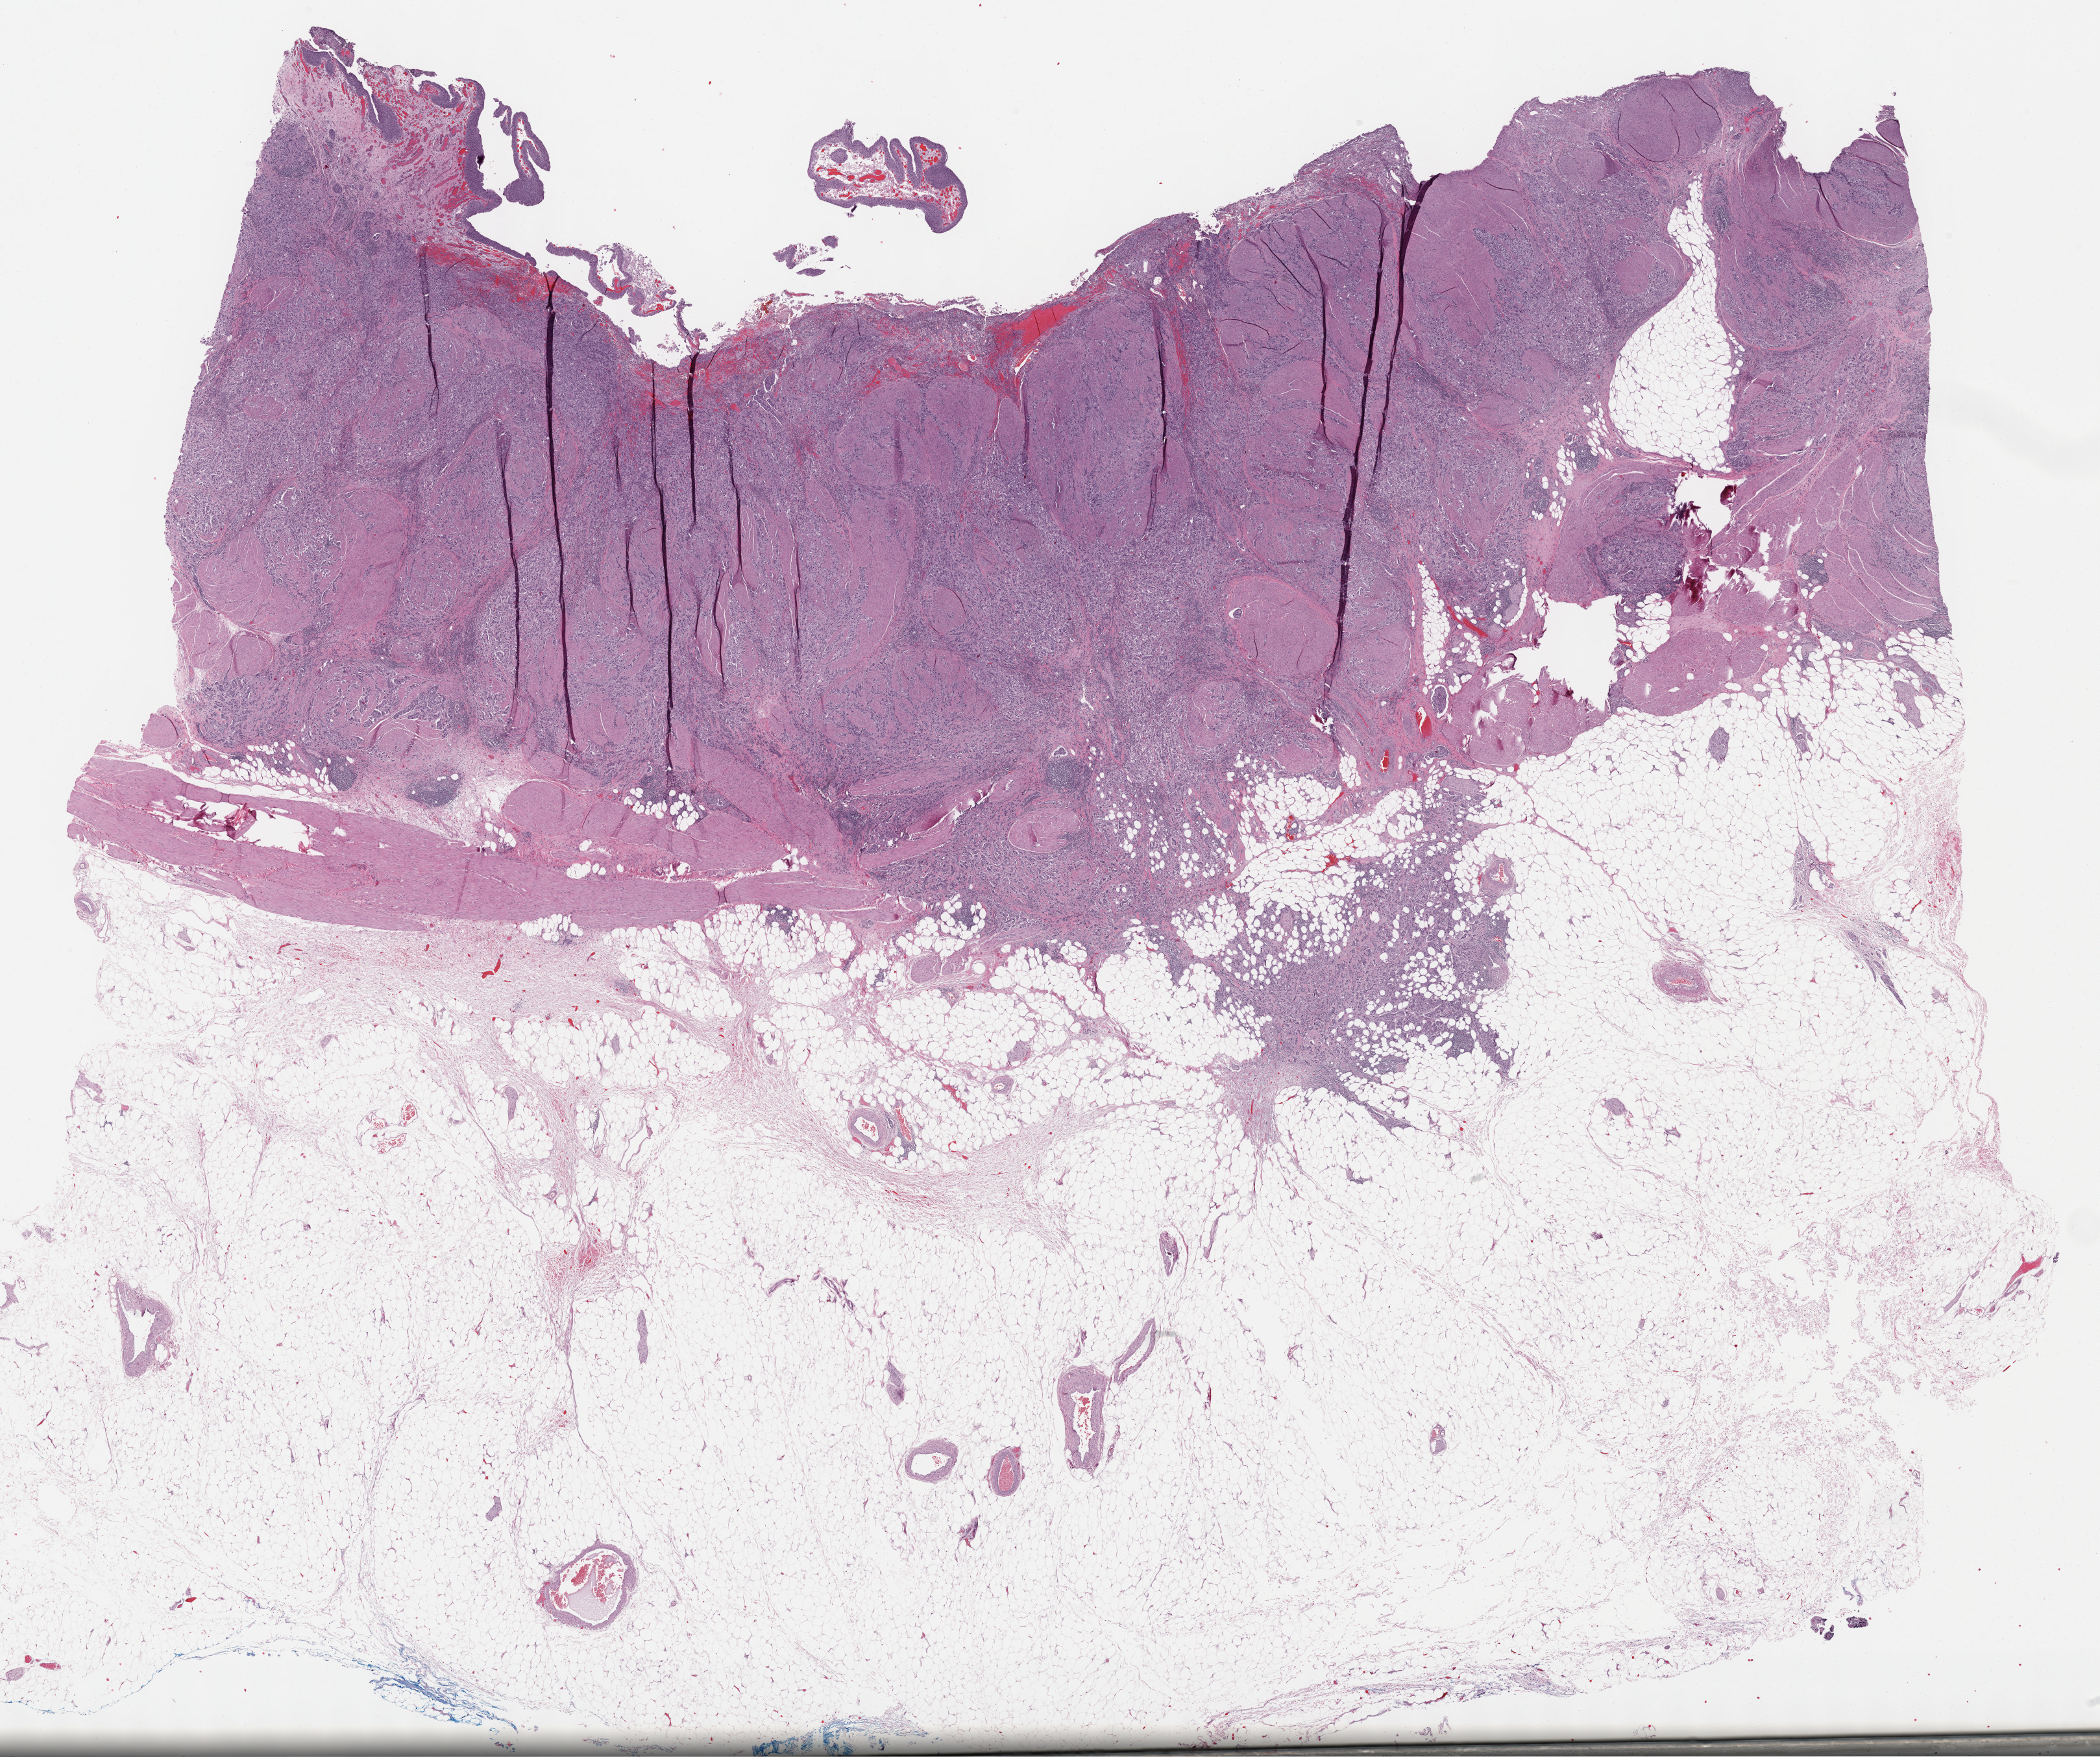
H&E whole-slide image — whole scanned area (about 26.2 x 21.9 mm, slide scanned at 40x) shown as a low-resolution overview, formalin-fixed paraffin-embedded (FFPE) diagnostic section, sample: primary tumour, bladder. Patient: male, age at initial diagnosis 62 years. Histologic grade: high grade.
• AJCC pathologic stage: III
• lymph nodes positive (case pathology): 0 of 7 examined
• pathologic diagnosis: Transitional cell carcinoma (lateral wall of bladder)